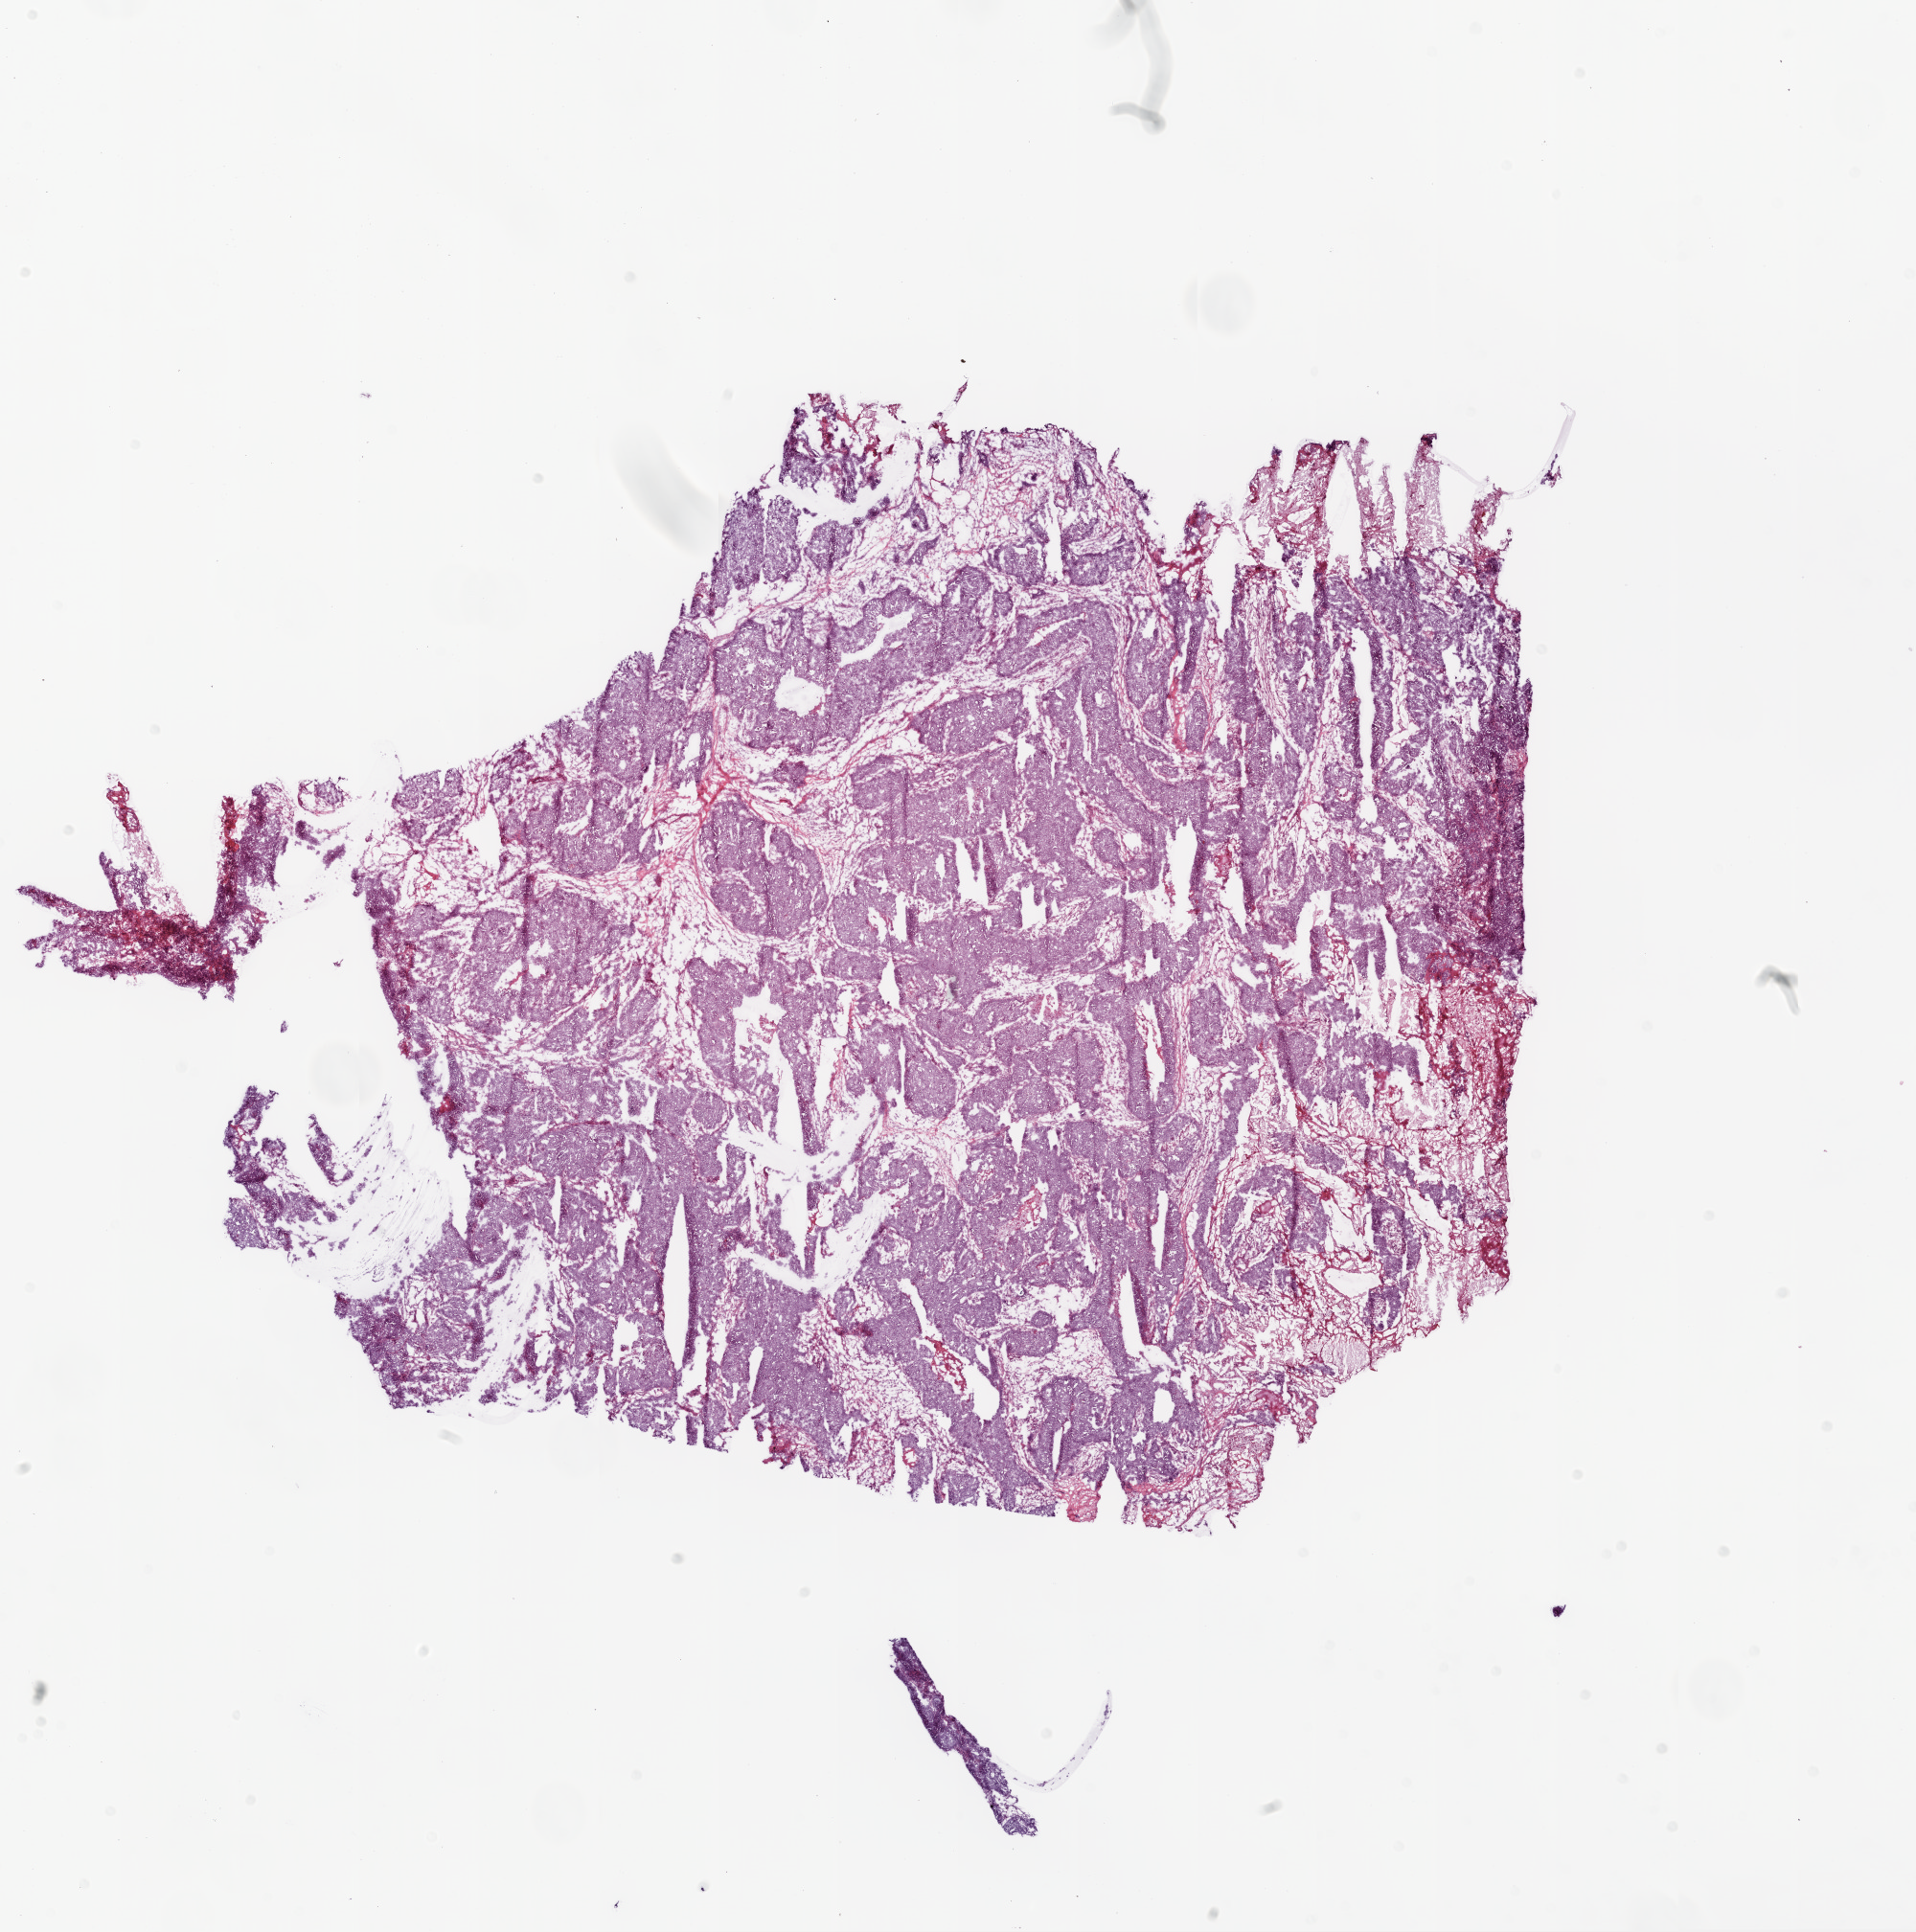
H&E-stained whole-slide image — a low-resolution overview of the entire scanned area, about 16.0 x 16.2 mm. Frozen section. Sample: primary tumour, ovary. Female, age 59 years at initial diagnosis. Histologic grade: G3 (poorly differentiated). Composition of this section per pathologist review: tumour cells 90%, tumour nuclei 90%, normal cells 0%, stromal cells 5%, necrosis 5%. Infiltration values recorded for this section: lymphocyte infiltration 0%, monocyte infiltration 0%, neutrophil infiltration 5%.
Laterality: bilateral. FIGO stage: IIIC. Pathologic diagnosis: Serous cystadenocarcinoma, NOS.